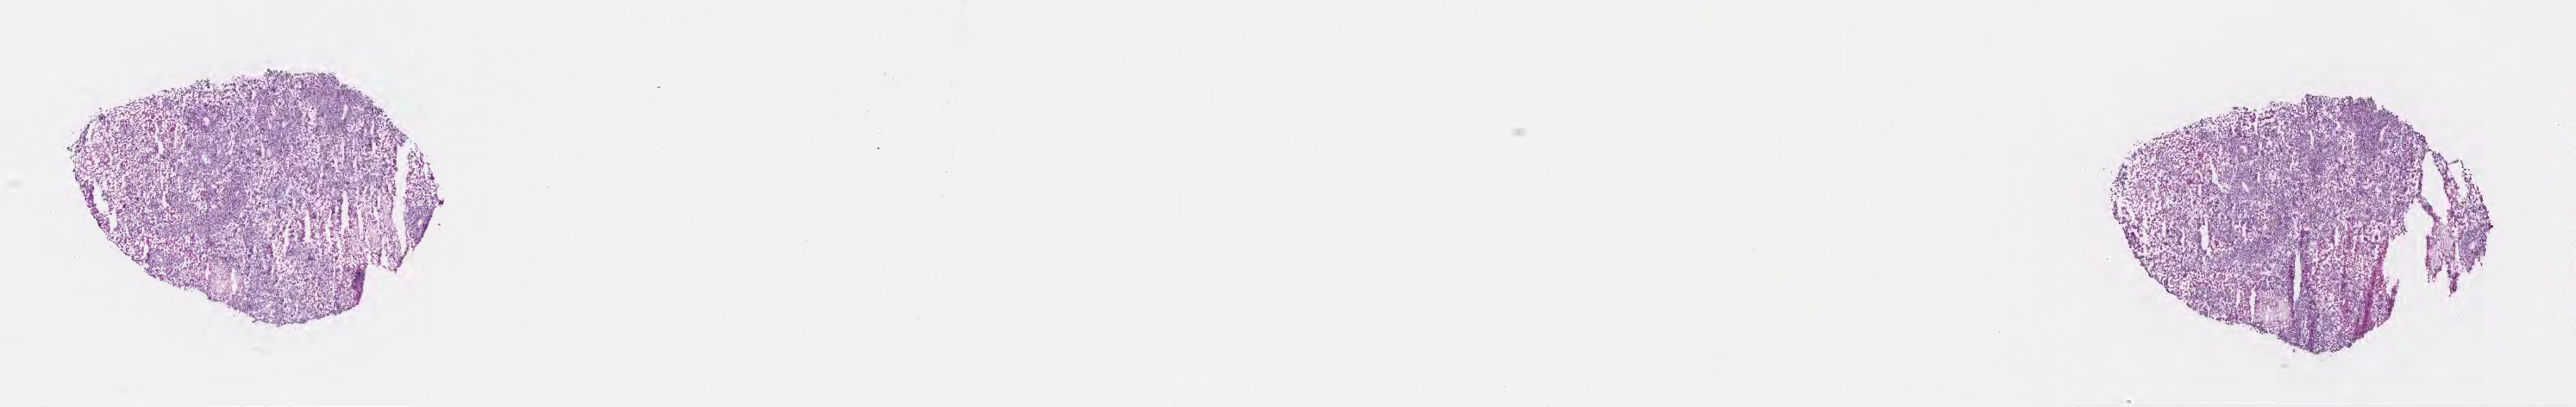
Digitized haematoxylin and eosin-stained section — low-resolution overview of the scanned area, about 24.2 x 3.8 mm. Frozen section (tissue freezing medium). Metastatic tumor tissue, resected from brain. Female patient; age at initial diagnosis 68 years. Slide review estimates, as recorded: tumor cells 80%, tumor nuclei 80%, stromal cells 8%, necrosis 12%, normal cells 0%. Infiltration values recorded for this section: lymphocyte infiltration 3%, monocyte infiltration 1%, neutrophil infiltration 2%.
* section: bottom of the tissue portion
* patient diagnosis (primary): Malignant melanoma, NOS